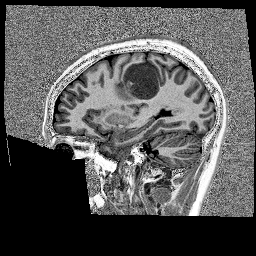
Brain MRI from a brain-tumour surgery series, one sagittal slice. Position 61 of 176 along the scan axis. 1 mm slice thickness. 256 × 256 image matrix, field of view 256 × 256 mm. From the clinical record (not read from this slice): histopathology: Glioblastoma; WHO grade: 4; IDH mutation: no.
Annotated regions visible in this slice (expert manual segmentation):
- tumour: bounding box <128,58,165,105> (left, top, right, bottom; pixels)